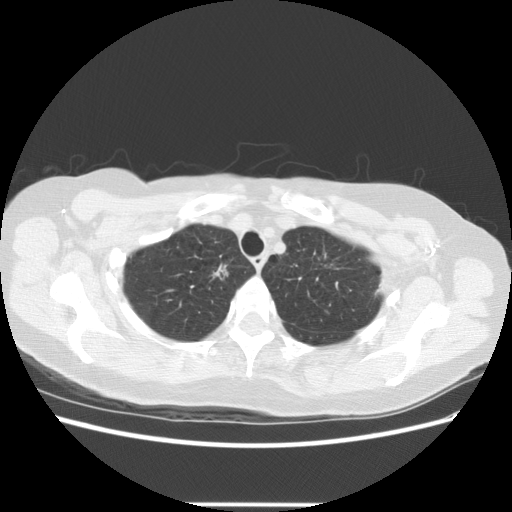
Low-dose screening chest CT, one axial slice; position 107 of 126 along the scan axis; 140 kVp; lung window (W 1500 / L -600 HU); 2.5 mm slice thickness; 512 × 512 image matrix, field of view 360 × 360 mm.
Annotated regions visible in this slice (outlined manually by an expert reader):
- lesion 1 (tumor, upper lobe of right lung): bounding box <213,262,229,280> (left, top, right, bottom; pixels)